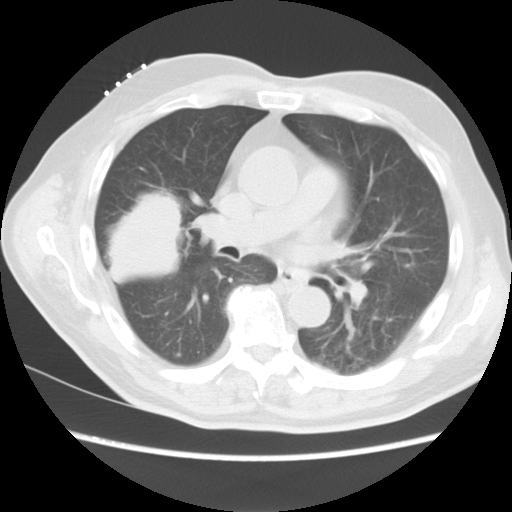
Chest CT, one axial slice; slice 5 of 15 in the series (ordered by position); lung window (W 1500 / L -600 HU); 5 mm slice thickness; 512 × 512 image matrix. Patient: male, 68 years. From the clinical record (not read from this slice): clinical TNM (as recorded): T4 N3 M0.
Outlined on this slice (bounding box drawn by a radiologist):
- lung tumour (recorded histology: squamous cell carcinoma): bounding box <98,187,187,290> (left, top, right, bottom; pixels)